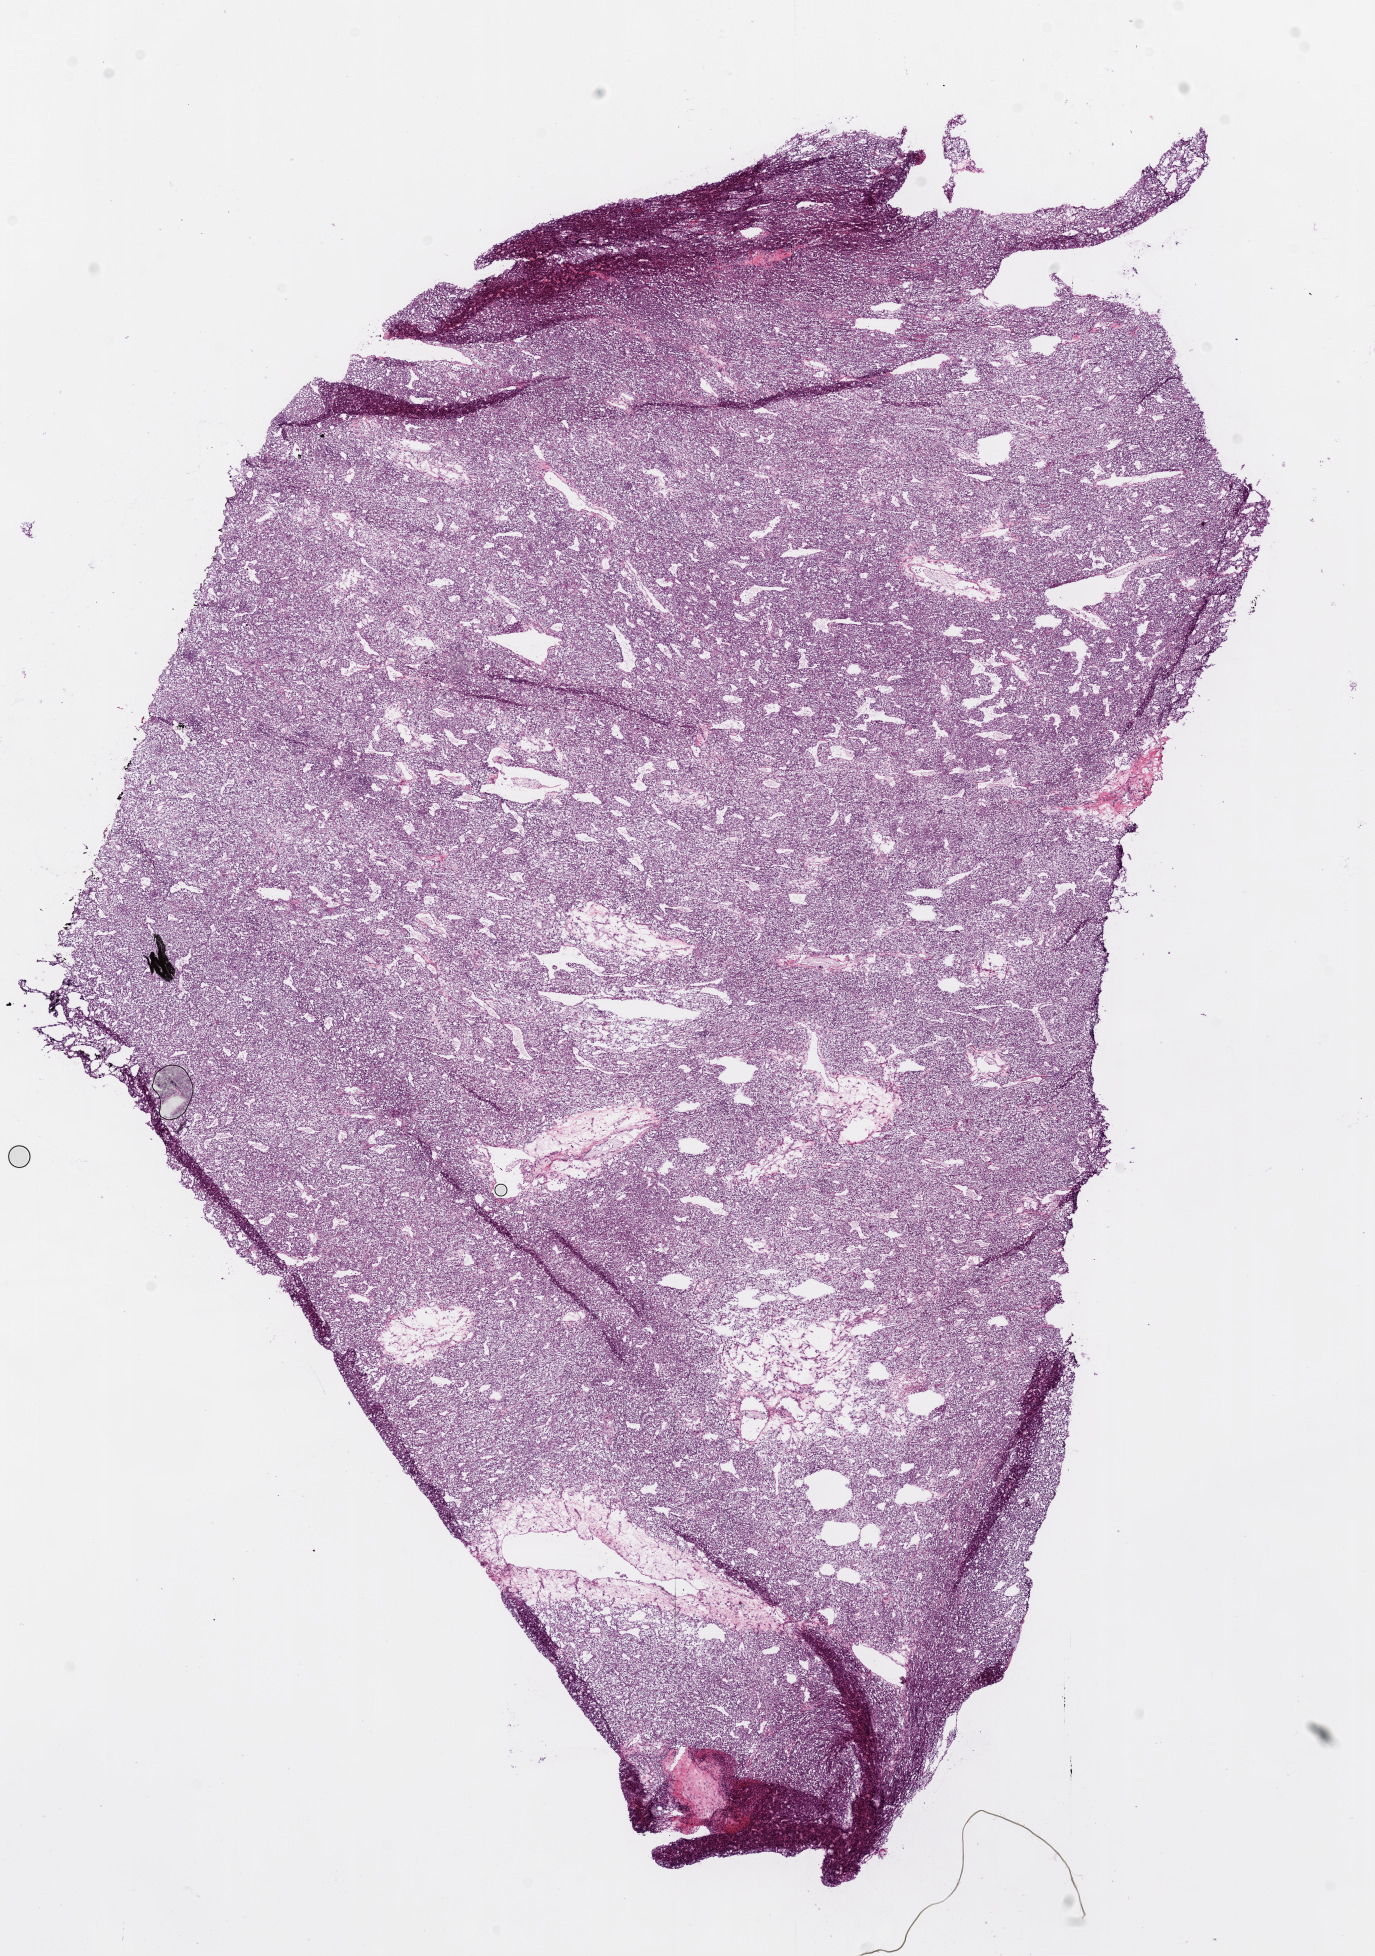
Whole-slide histology image, H&E-stained, low-resolution overview of the scanned area, about 11.0 x 15.7 mm (acquisition: 20x scan), frozen section from the bottom of the tissue portion, sample: primary tumour, kidney. Male, age 75 years at initial diagnosis. Histologic grade: G2 (moderately differentiated). Composition of this section per pathologist review: tumour cells 95%, tumour nuclei 85%, normal cells 0%, stromal cells 5%, necrosis 0%.
• pathologic diagnosis: Clear cell adenocarcinoma, NOS
• AJCC pathologic stage: I
• laterality: right